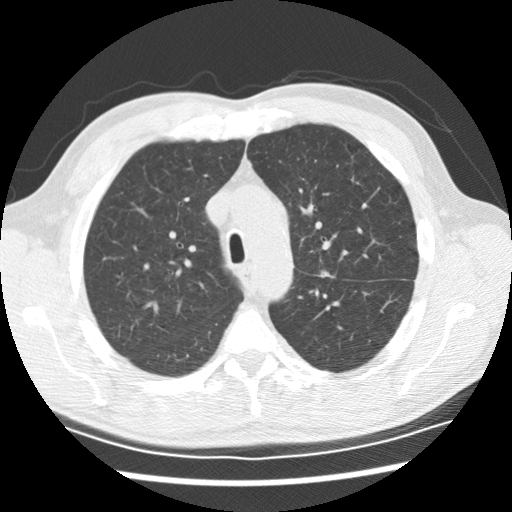
Low-dose screening chest CT, axial slice. Second screening round (one year after baseline). Lung window (W 1500 / L -600 HU). Male, age 59 years at enrolment. Current smoker at enrolment.
Expert-annotated lung lesion, bounding box [x1, y1, x2, y2] px = [306, 258, 344, 294]. Reader record for this screening exam (exam-level; its link to the box is not recorded): non-calcified nodule or mass ≥4 mm, left upper lobe, 8 × 7 mm, spiculated (stellate) margins, soft tissue attenuation, pre-existing on the prior screen: yes; interval growth: yes. Lung cancer was diagnosed 251 days after this screen: adenocarcinoma, NOS, left upper lobe, left lower lobe, poorly differentiated (G3), stage IV (AJCC 6th edition).